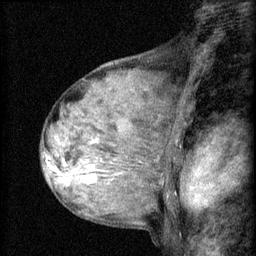
Breast MRI (dynamic contrast-enhanced), one sagittal slice. Position 40 of 60 along the scan axis. 3 images stored at this slice position (order not interpretable as contrast timing). 1.5 T. TE 4.2 ms, TR 8.2 ms. 2 mm slice thickness. 256 × 256 image matrix, field of view 180 × 180 mm. Patient: female, 48 years.
Outlined on this slice (semi-automatically segmented with operator editing):
- analysis volume of interest (the breast-tissue region the enhancement analysis was run in; not a lesion): bounding box (x1, y1, x2, y2) in pixels: (54, 138, 133, 191)
- tumour enhancement mask (voxels above the 70 % enhancement threshold inside the analysis volume of interest): (54, 160, 93, 181)